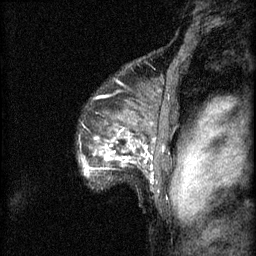
Breast MRI (dynamic contrast-enhanced), one sagittal slice; position 53 of 60 along the scan axis; 3 images stored at this slice position (order not interpretable as contrast timing); 1.5 T; TE 4.2 ms, TR 8.2 ms; 2 mm slice thickness; 256 × 256 image matrix, field of view 180 × 180 mm. Female patient, age 48 years.
Structures marked on this image (semi-automatic segmentation, software-assisted and operator-edited):
- analysis volume of interest (the breast-tissue region the enhancement analysis was run in; not a lesion): bounding box (x1, y1, x2, y2) in pixels: (86, 138, 153, 185)
- tumour enhancement mask (voxels above the 70 % enhancement threshold inside the analysis volume of interest): (86, 156, 111, 173)